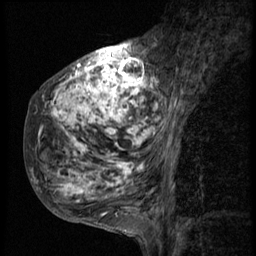
Breast MRI (dynamic contrast-enhanced), one sagittal slice. Position 19 of 58 along the scan axis. 3 images stored at this slice position (order not interpretable as contrast timing). 1.5 T. TE 4.2 ms, TR 9 ms. 256 × 256 image matrix, field of view 180 × 180 mm. Patient: female, 50 years. Case-level facts recorded for this patient, not image findings: setting: breast cancer imaged before/during neoadjuvant chemotherapy; receptor status: triple-negative.
Outlined on this slice (semi-automatically segmented with operator editing):
- analysis volume of interest (the breast-tissue region the enhancement analysis was run in; not a lesion): bounding box (x1, y1, x2, y2) in pixels: (25, 48, 186, 214)
- tumour enhancement mask (voxels above the 140 % enhancement threshold inside the analysis volume of interest): (30, 48, 186, 202)